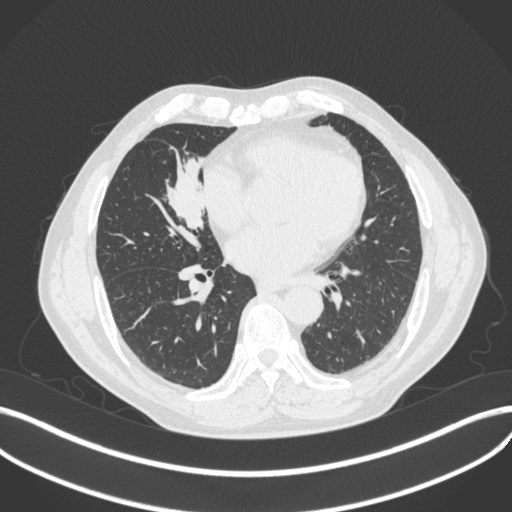
Chest CT, one axial slice; slice 174 of 429 in the series (ordered by position); reconstruction kernel B31f; lung window (W 1500 / L -600 HU); 512 × 512 image matrix, field of view 400 × 400 mm. Patient: male, 61 years. Case-level facts recorded for this patient, not image findings: clinical TNM (as recorded): T2b N1 M0.
Structures marked on this image (bounding box drawn by a radiologist):
- lung tumour (recorded histology: squamous cell carcinoma): bounding box <162,146,209,231> (left, top, right, bottom; pixels)